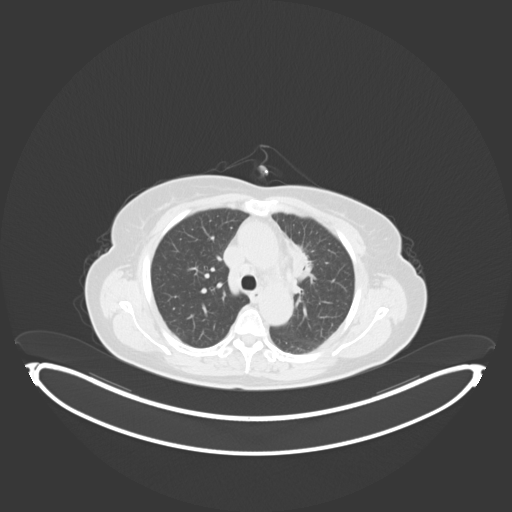
Chest CT, one axial slice; reconstruction kernel B30f; 120 kVp; lung window (W 1500 / L -600 HU); 3 mm slice thickness; 512 × 512 image matrix, field of view 500 × 500 mm. Patient: female, 65 years. Case-level facts recorded for this patient, not image findings: clinical TNM (as recorded): T2a N0 M0; histopathological grade: G2-3.
Structures marked on this image (rectangle marked by the reading radiologist):
- lung tumour (recorded histology: adenocarcinoma): box from (x=287, y=236) to (x=314, y=282) px